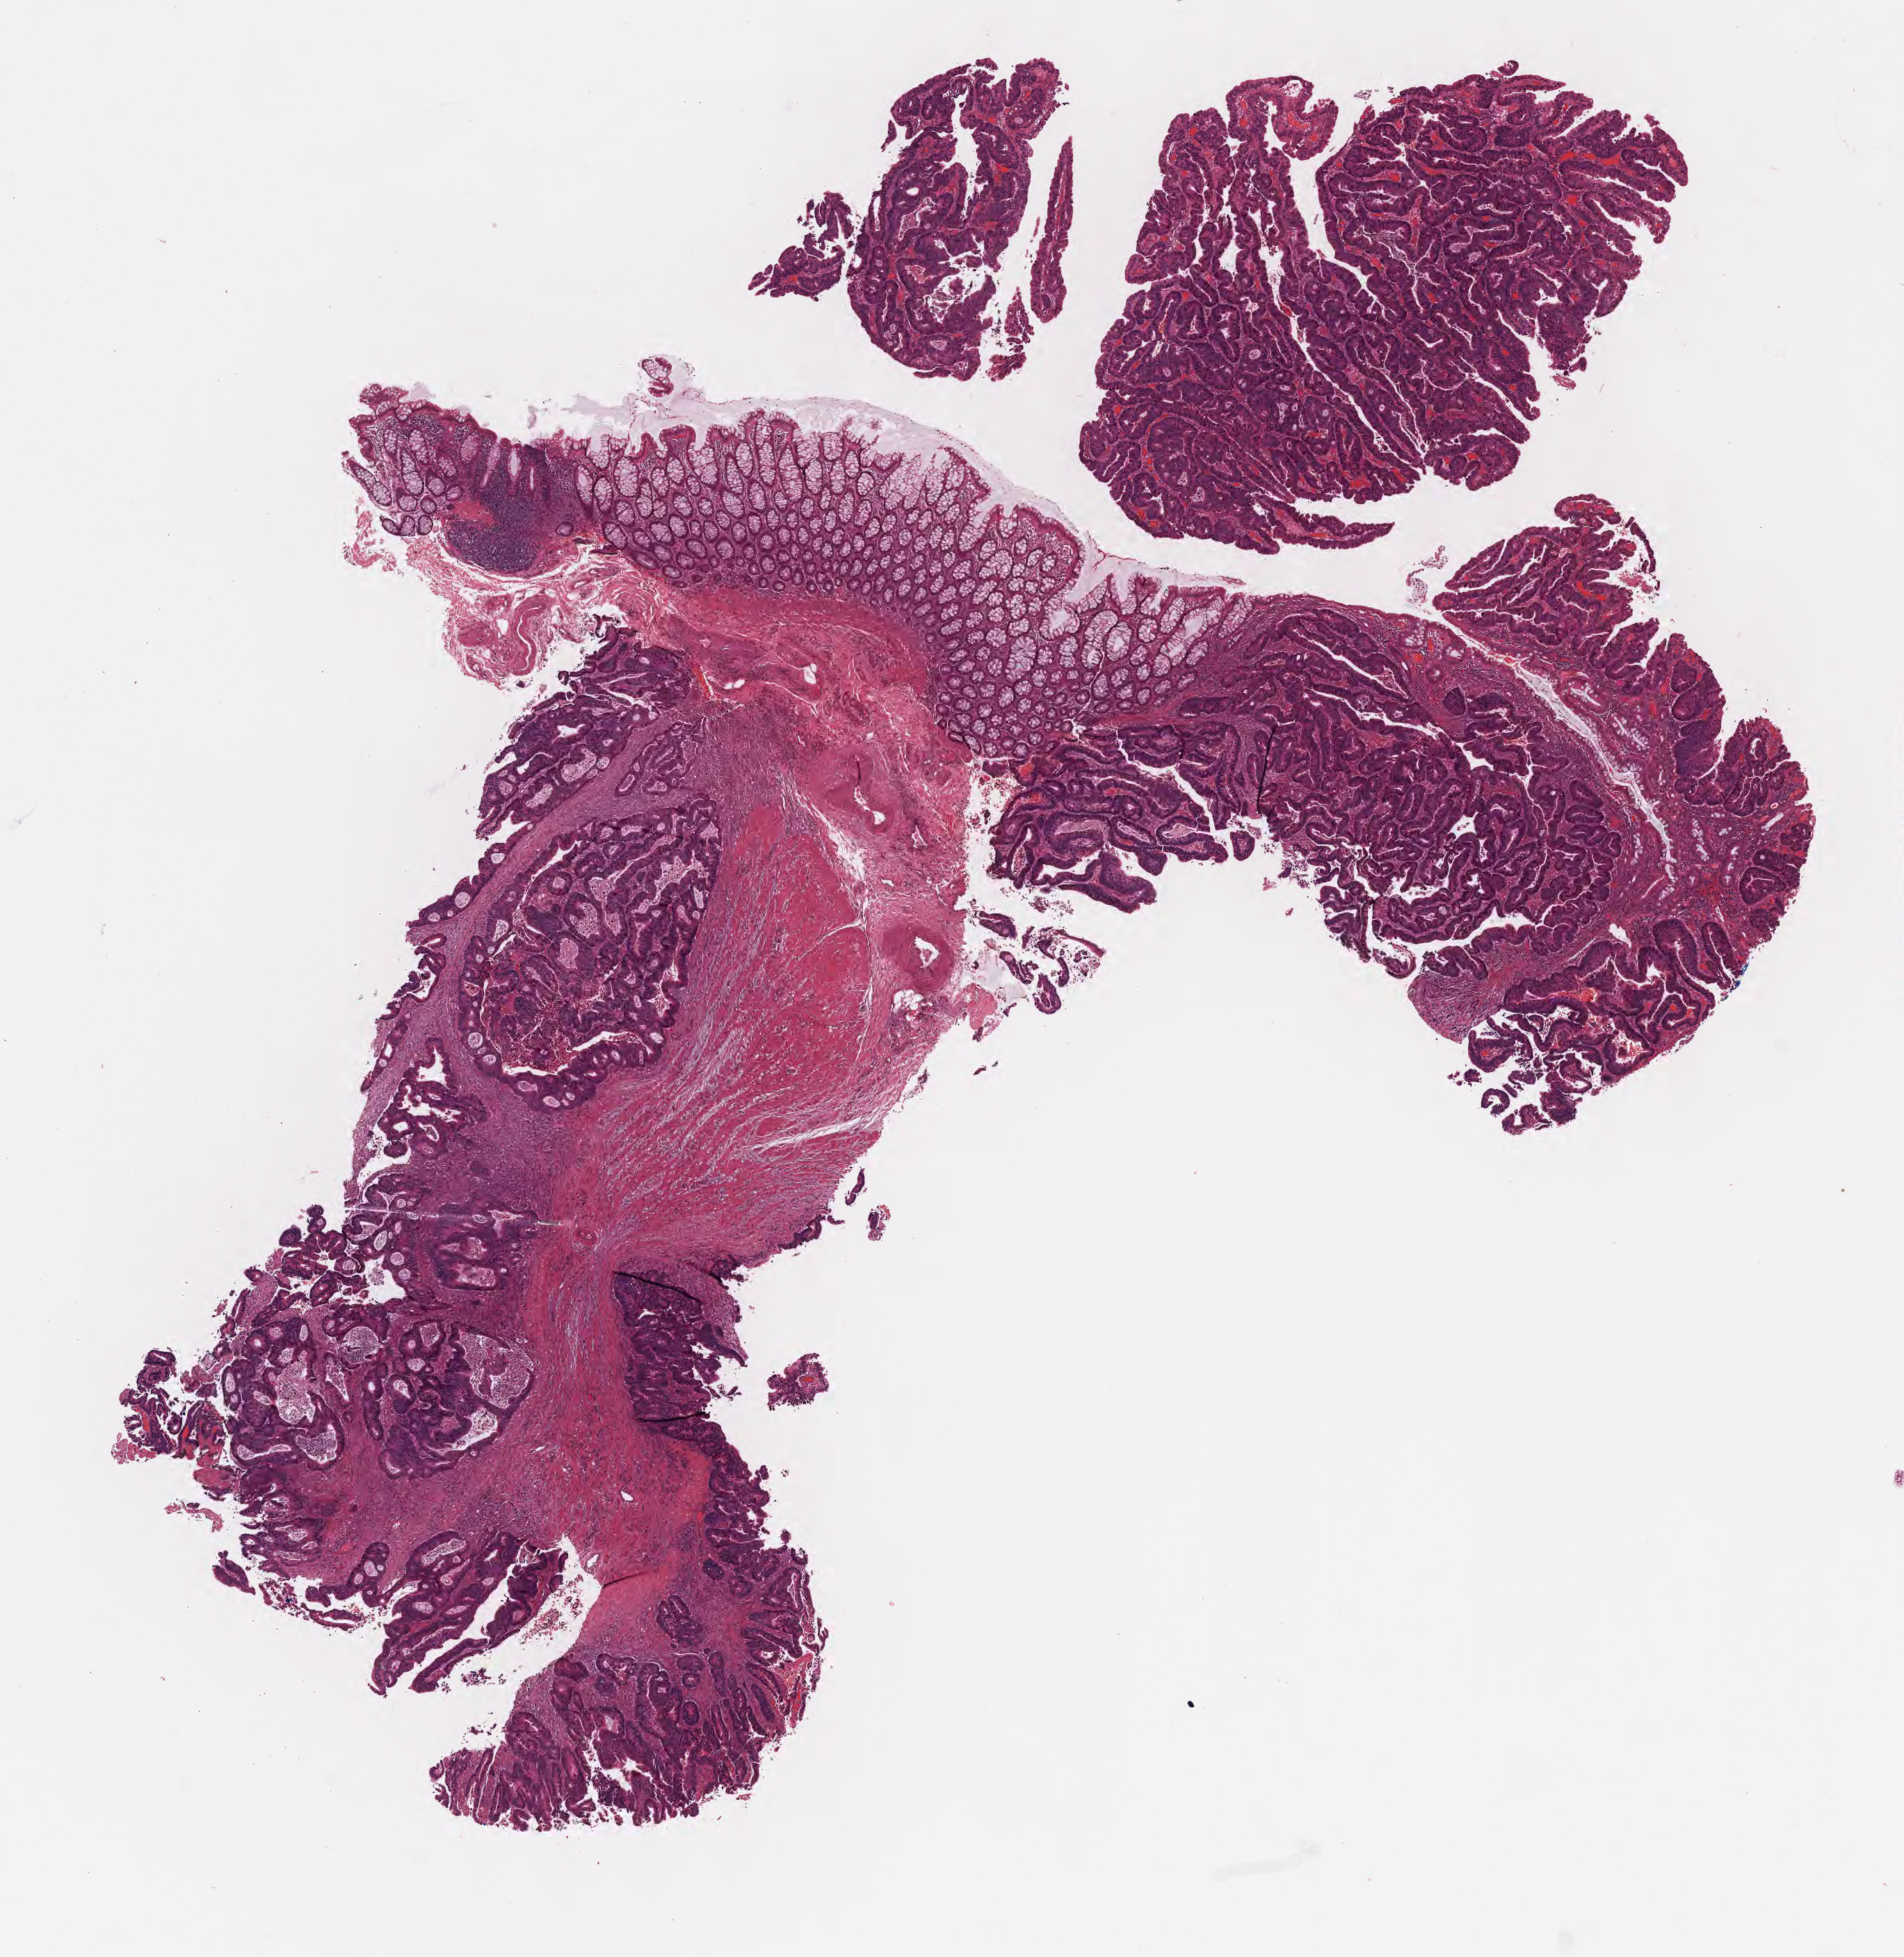
H&E whole-slide image, a low-resolution overview of the entire scanned area, about 11.1 x 11.4 mm; formalin-fixed, paraffin-embedded (FFPE) tissue; primary tumor; site: sigmoid colon. Patient: female, age at initial diagnosis 72 years.
Diagnosis: Adenocarcinoma, NOS.